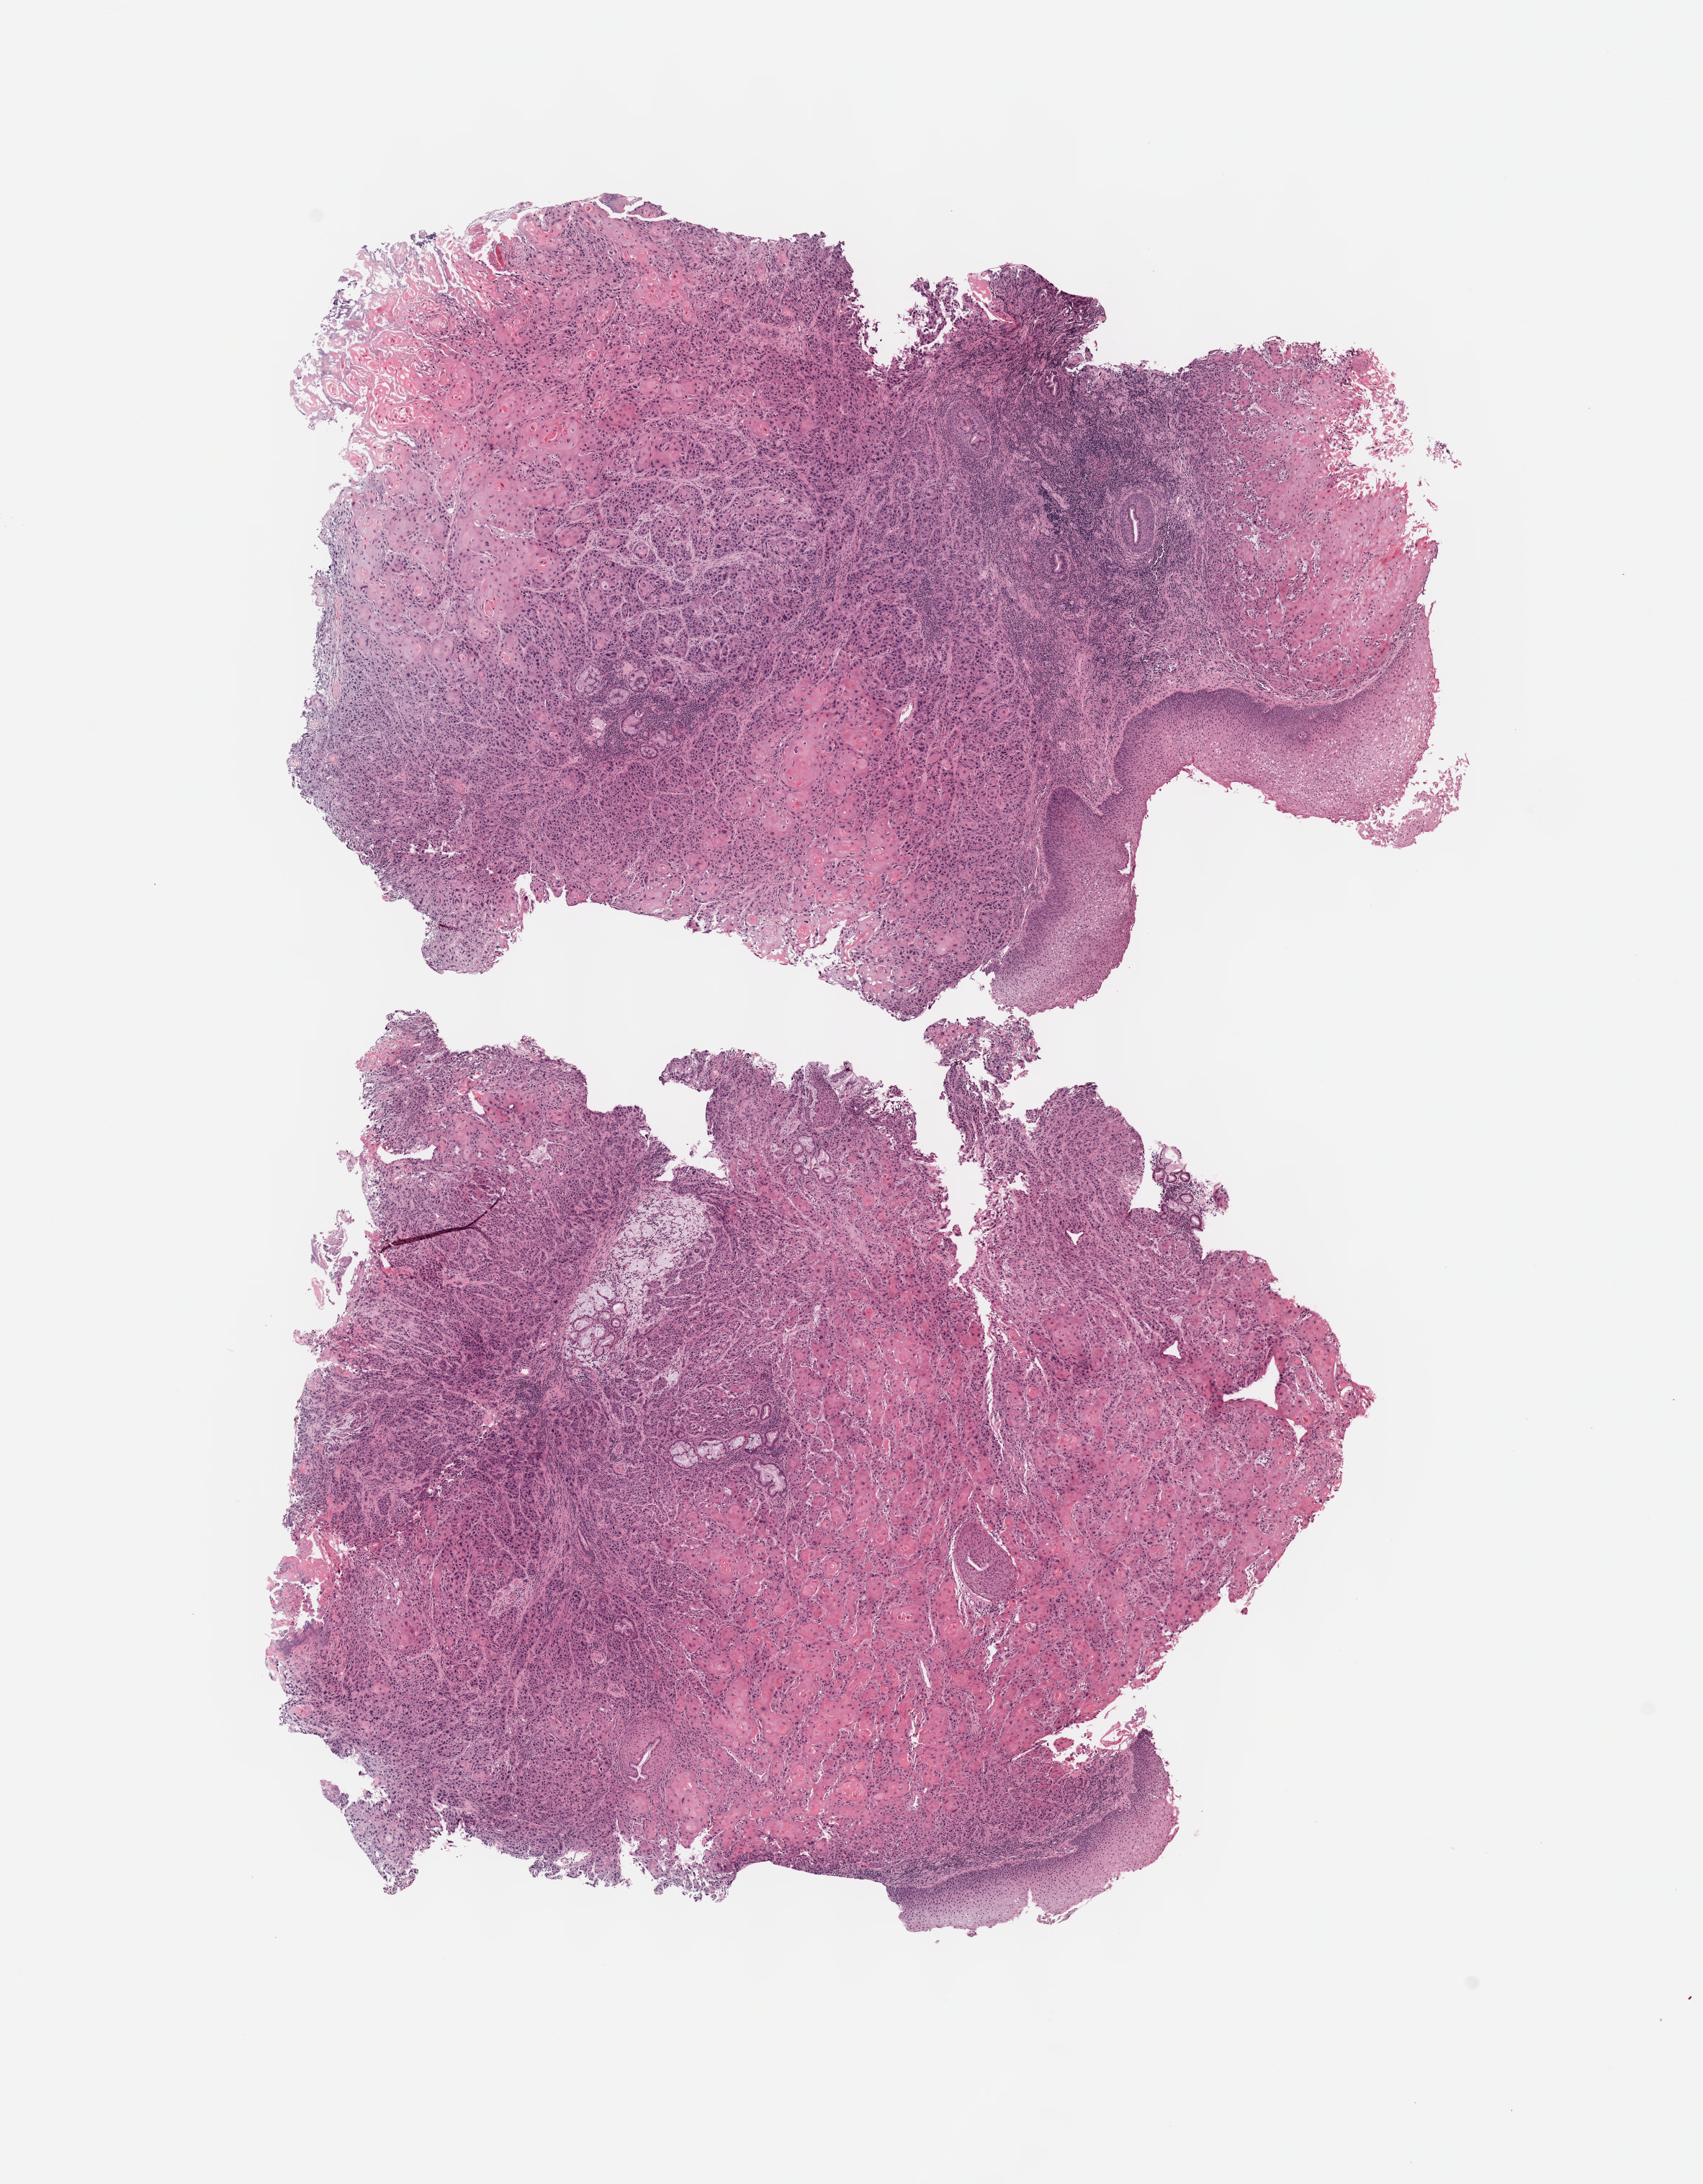
Digitized H&E tissue section (whole slide) — shown as a low-resolution overview of the whole scanned area (about 9.6 x 12.3 mm, acquisition: 40x scan), formalin-fixed paraffin-embedded (FFPE) diagnostic section, sample: primary tumour, head and neck. Male patient; age at initial diagnosis 51 years. Histologic grade: G2 (moderately differentiated).
- laterality: midline
- AJCC pathologic stage: IVA
- pathologic diagnosis: Squamous cell carcinoma, keratinizing, NOS (larynx, NOS)